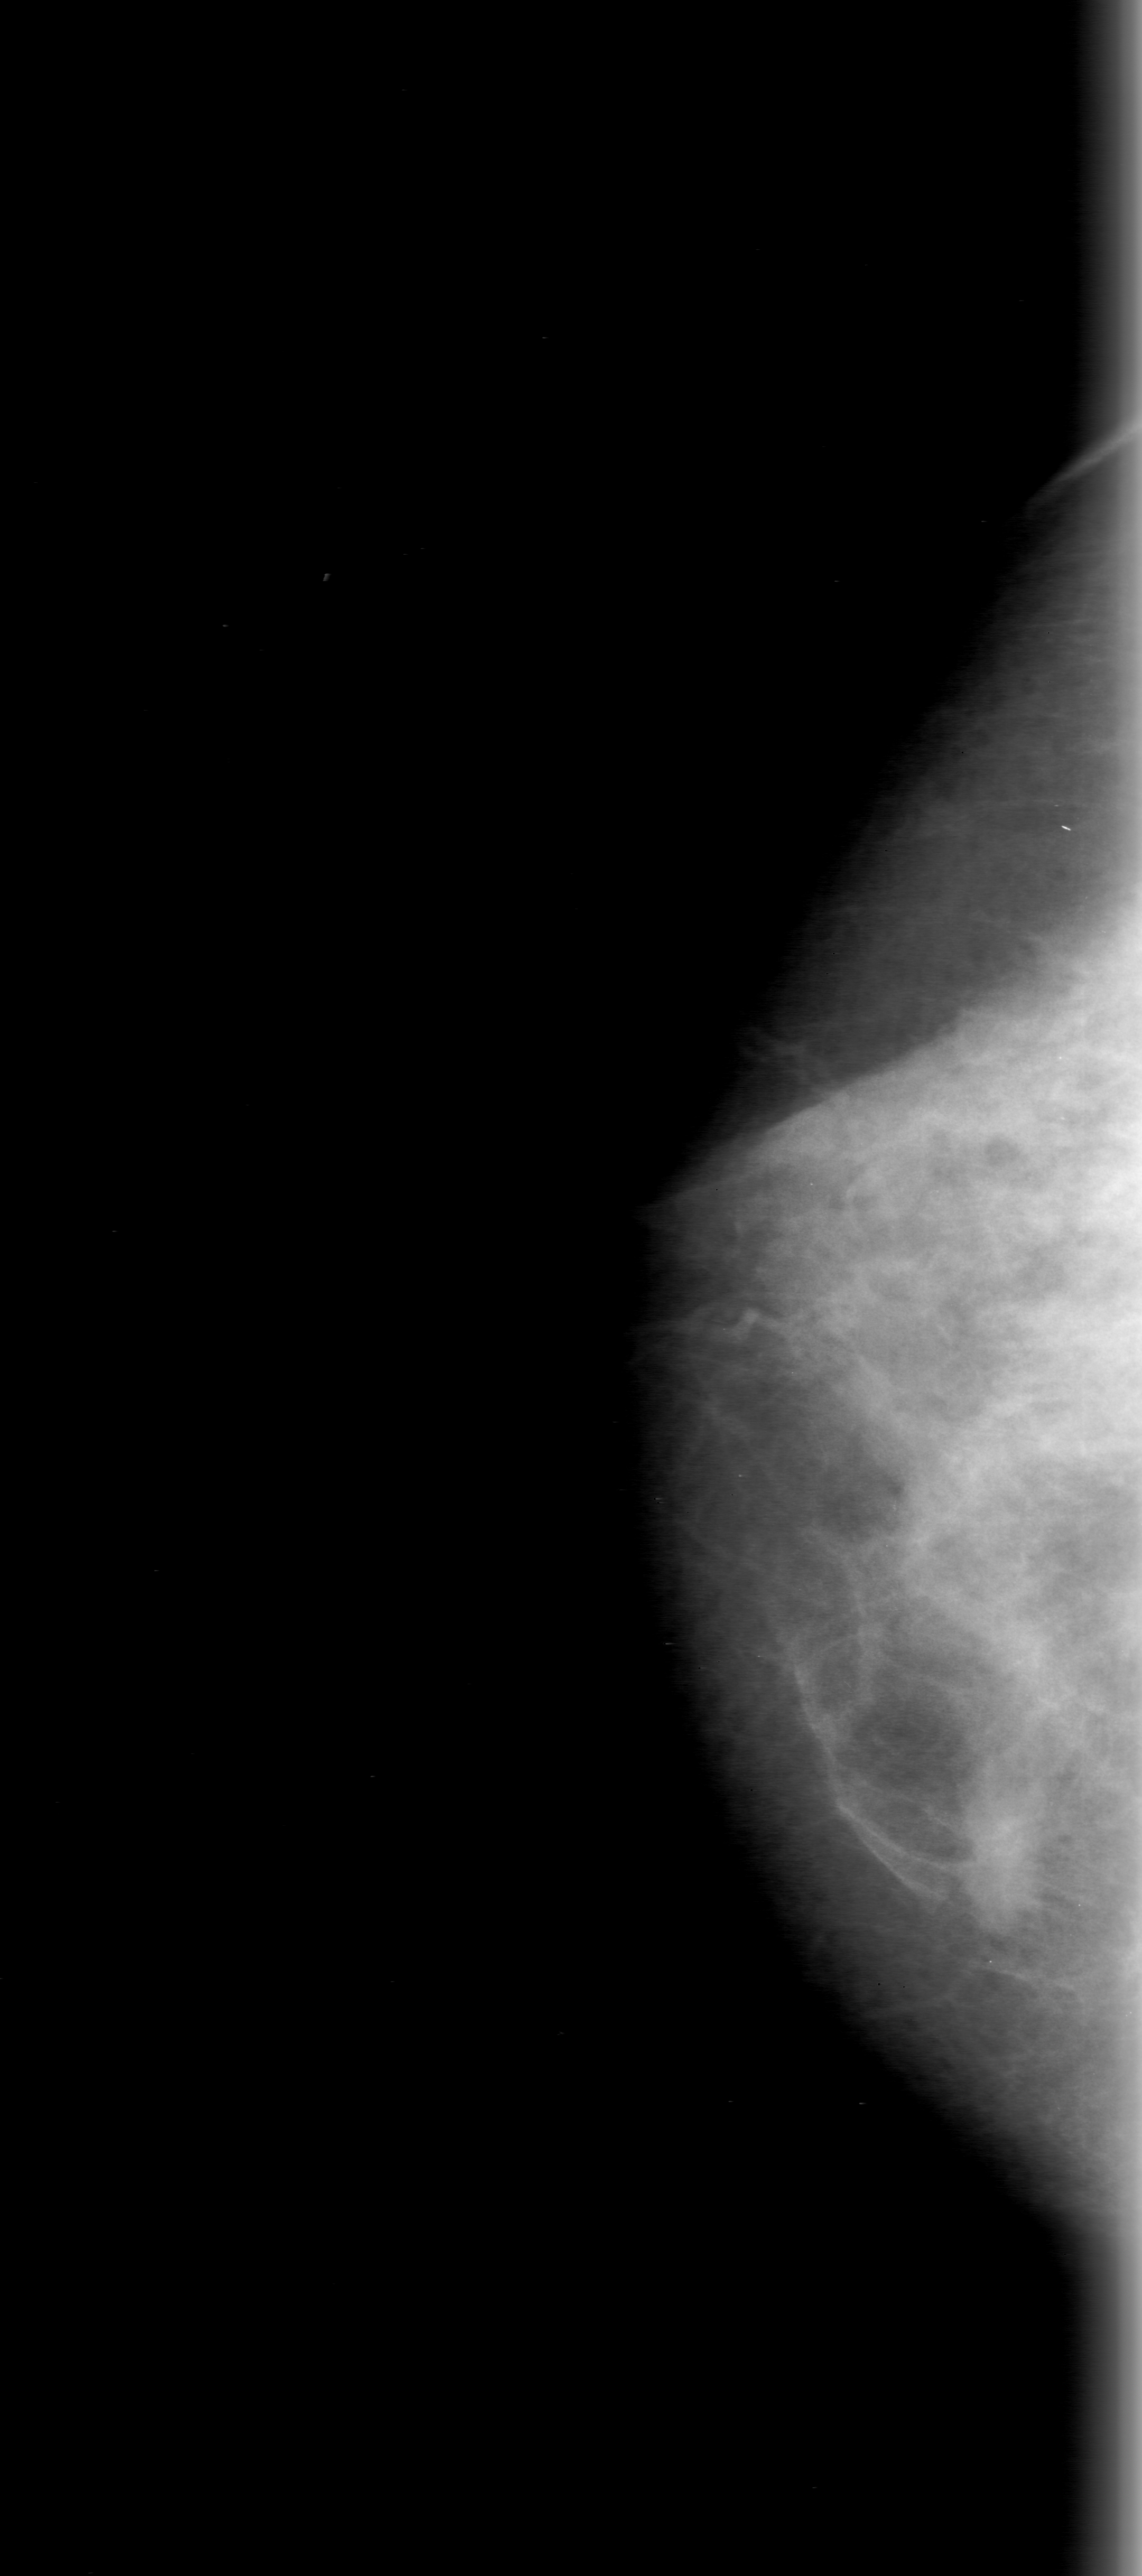
Digitized screen-film mammogram. Right breast. CC view. 1142 × 2576 image matrix.
Expert-marked regions of interest on this image (one box per marked abnormality):
- mass, shape irregular, margins ill defined; BI-RADS assessment category 0 (incomplete: needs additional imaging); pathology (as recorded): malignant: bounding box [x1, y1, x2, y2] px = [929, 1774, 1071, 1936]